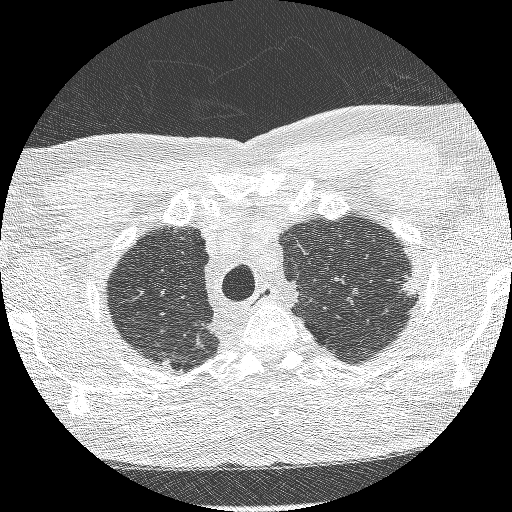
Low-dose screening chest CT, axial slice. Third screening round (two years after baseline). Lung window (W 1500 / L -600 HU). Lung (sharp) reconstruction kernel (BONE). Slice 240 of 275 in the series. 512 × 512 image matrix, field of view 330 × 330 mm. Male participant, aged 66 years at enrolment.
- Expert-annotated lung lesion, box from (x=387, y=269) to (x=431, y=314) px.
- The exam's reader record, not a measurement of the box and not confirmed to be the same lesion: non-calcified nodule or mass ≥4 mm, left lower lobe, 15 × 9 mm, spiculated (stellate) margins, soft tissue attenuation, pre-existing on the prior screen: yes; interval growth: yes.
- Official screen result: positive, other.
- Participant outcome: lung cancer diagnosed 225 days after this screen — adenocarcinoma, NOS, left upper lobe, poorly differentiated (G3), stage IB (AJCC 6th edition), 16 mm at pathology.